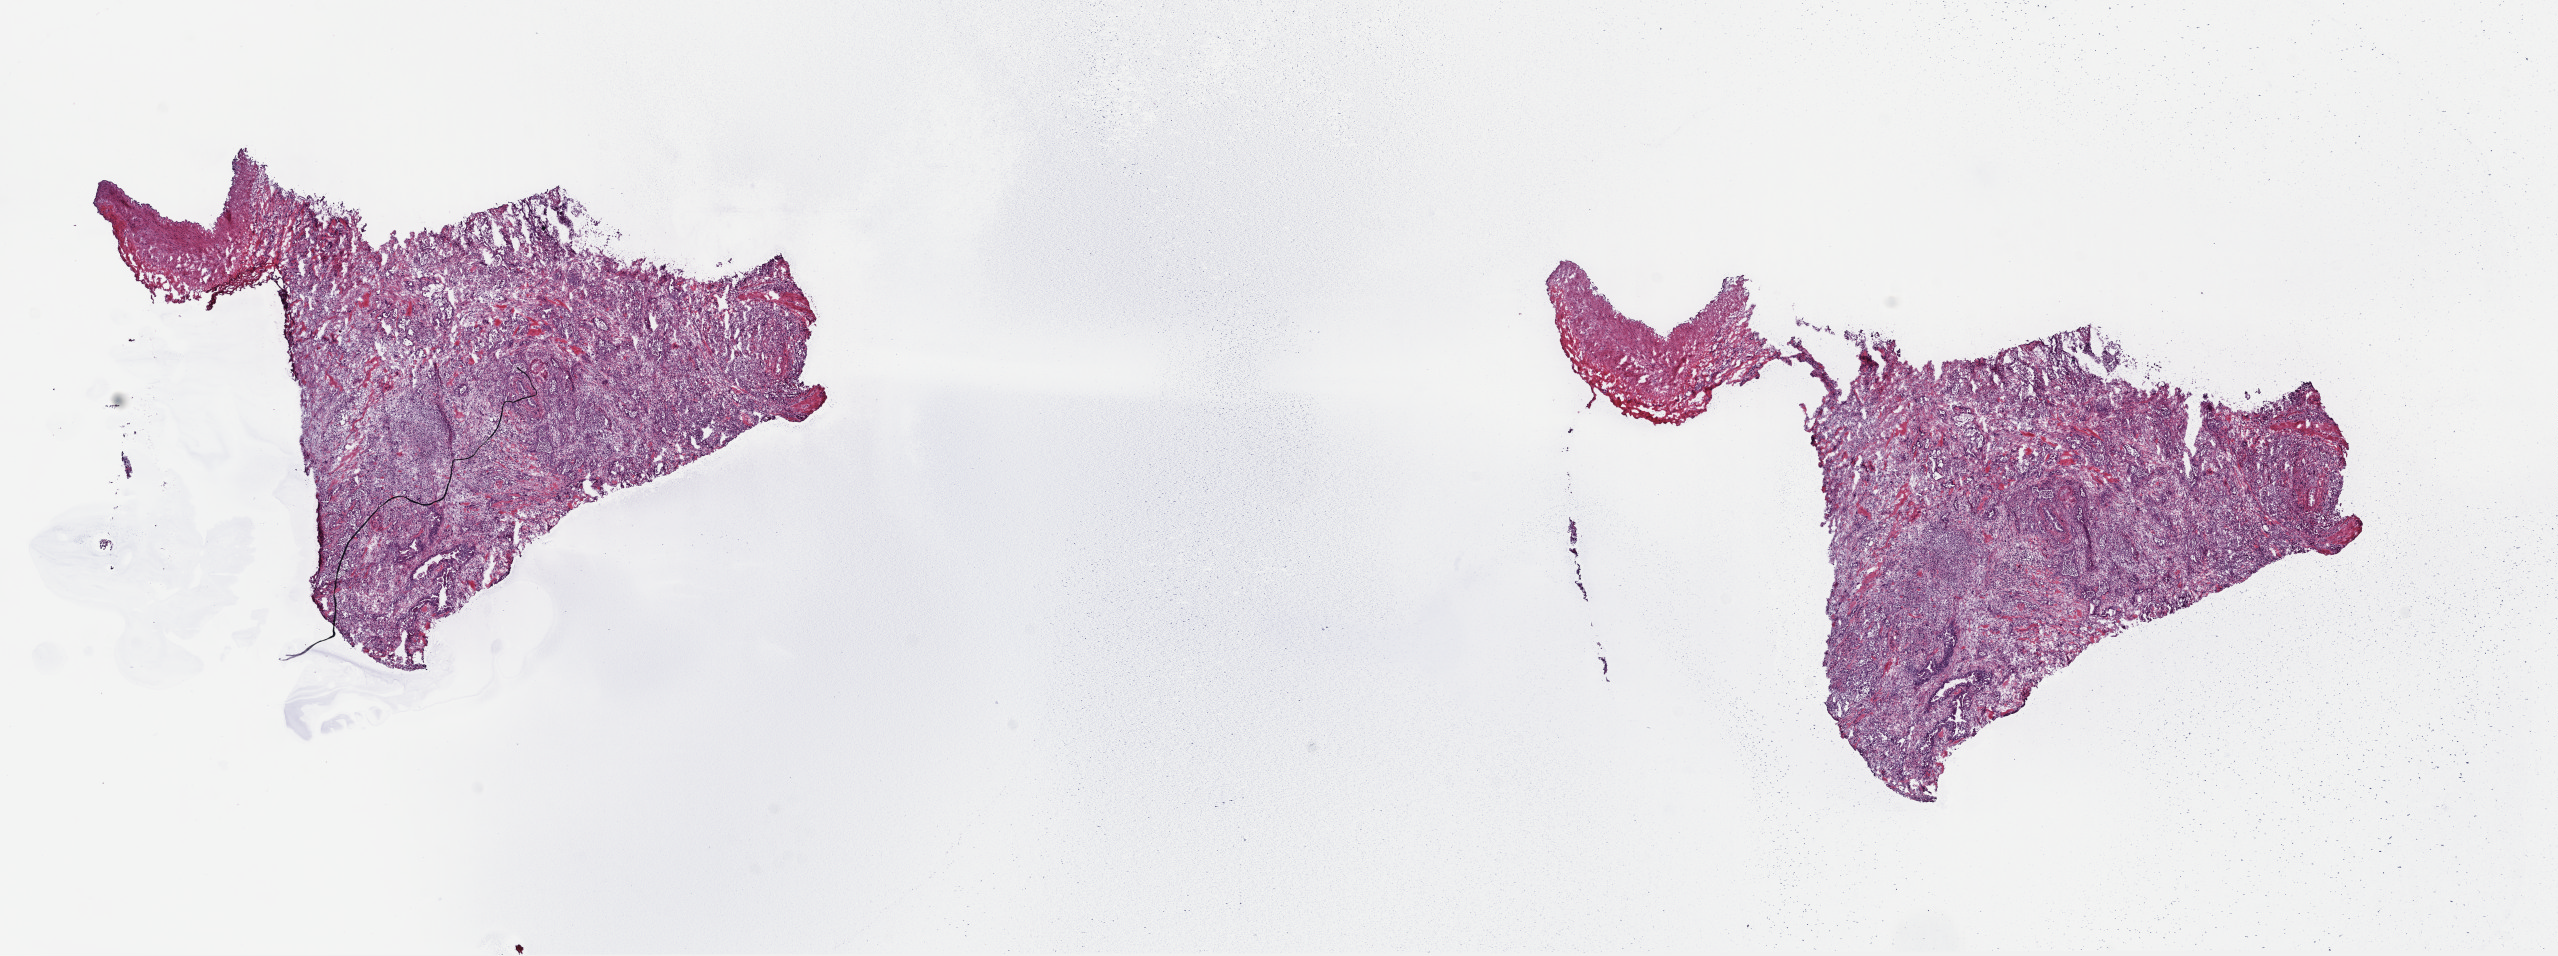
Digitized Hematoxylin and eosin (H&E) stained tissue section (whole slide), whole scanned area (about 20.1 x 7.5 mm, acquisition: 40x scan) shown as a low-resolution overview; frozen section from the top of the tissue portion; sample: primary tumour, pancreas. Patient: female, age at initial diagnosis 48 years. Histologic grade: G2 (moderately differentiated). Slide review estimates, as recorded: tumour cells 25%, tumour nuclei 65%, normal cells 0%, stromal cells 55%, necrosis 20%. Infiltration values recorded for this section: lymphocyte infiltration 8%, monocyte infiltration 5%, neutrophil infiltration 12%.
Pathologic diagnosis: Infiltrating duct carcinoma, NOS (head of pancreas). AJCC pathologic stage: IIA.